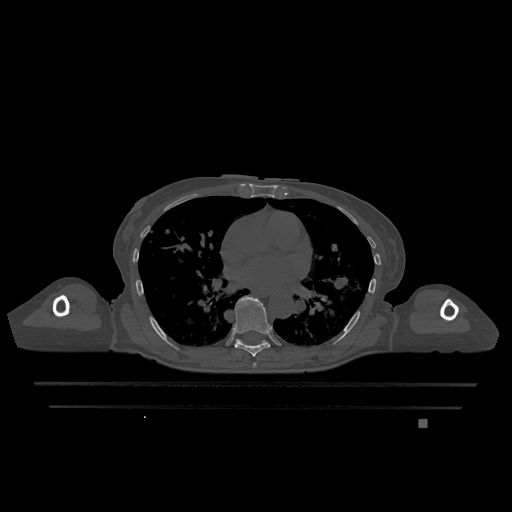
CT including the spine, one axial slice. Slice 731 of 1317 in the series (ordered by position). Bone window (W 1800 / L 400 HU). 0.5 mm slice thickness. 512 × 512 image matrix, field of view 500 × 500 mm. Female patient, age 74 years. From the clinical record (not read from this slice): primary cancer: lung; vertebrae with lytic lesions (as recorded): T1, T4, T5, T6, L4, L5.
Structures marked on this image (semi-automatic segmentation, software-assisted and operator-edited):
- T6 vertebra: bounding box [x1, y1, x2, y2] px = [253, 362, 257, 367]
- T7 vertebra: [235, 296, 270, 357]
- T9 vertebra: [236, 339, 266, 343]